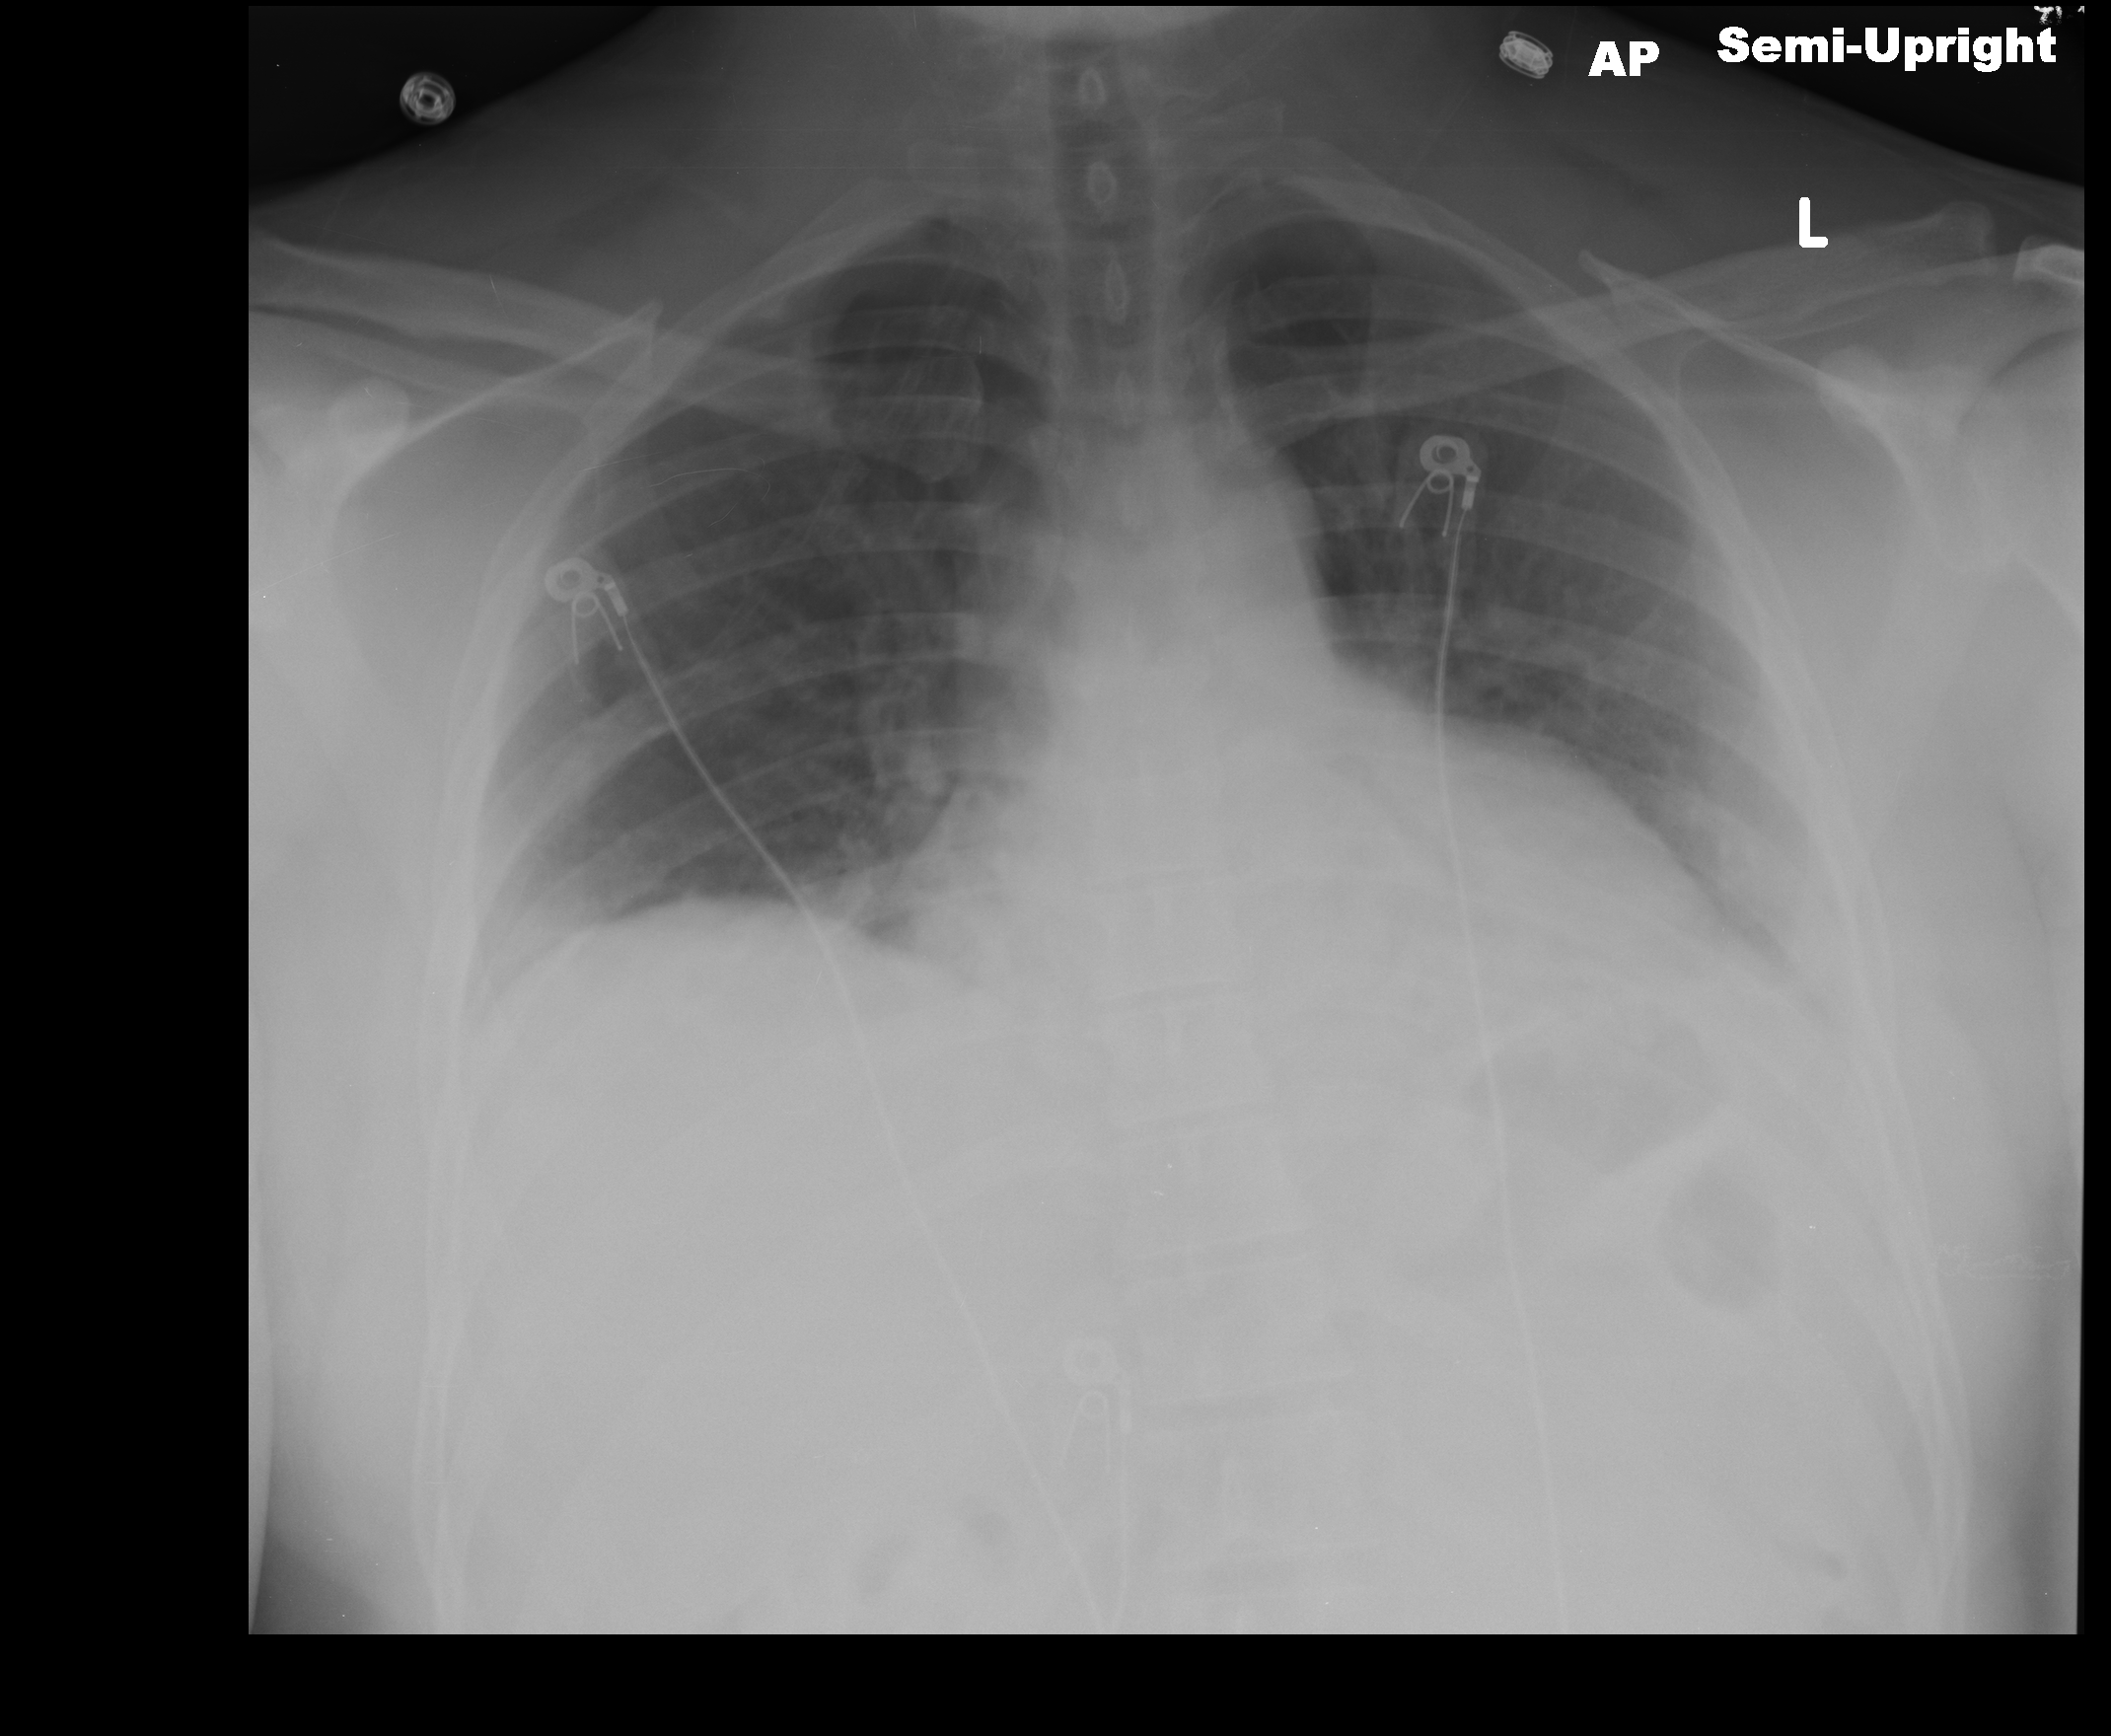
Chest radiograph. Male patient, age 44 years; imaged 0 days after the COVID-19 diagnosis.
Radiologist key findings (as recorded): patchy increased opacity in the lower lobes bilaterally, more pronounced on the lateral view. Small pleural effusions.